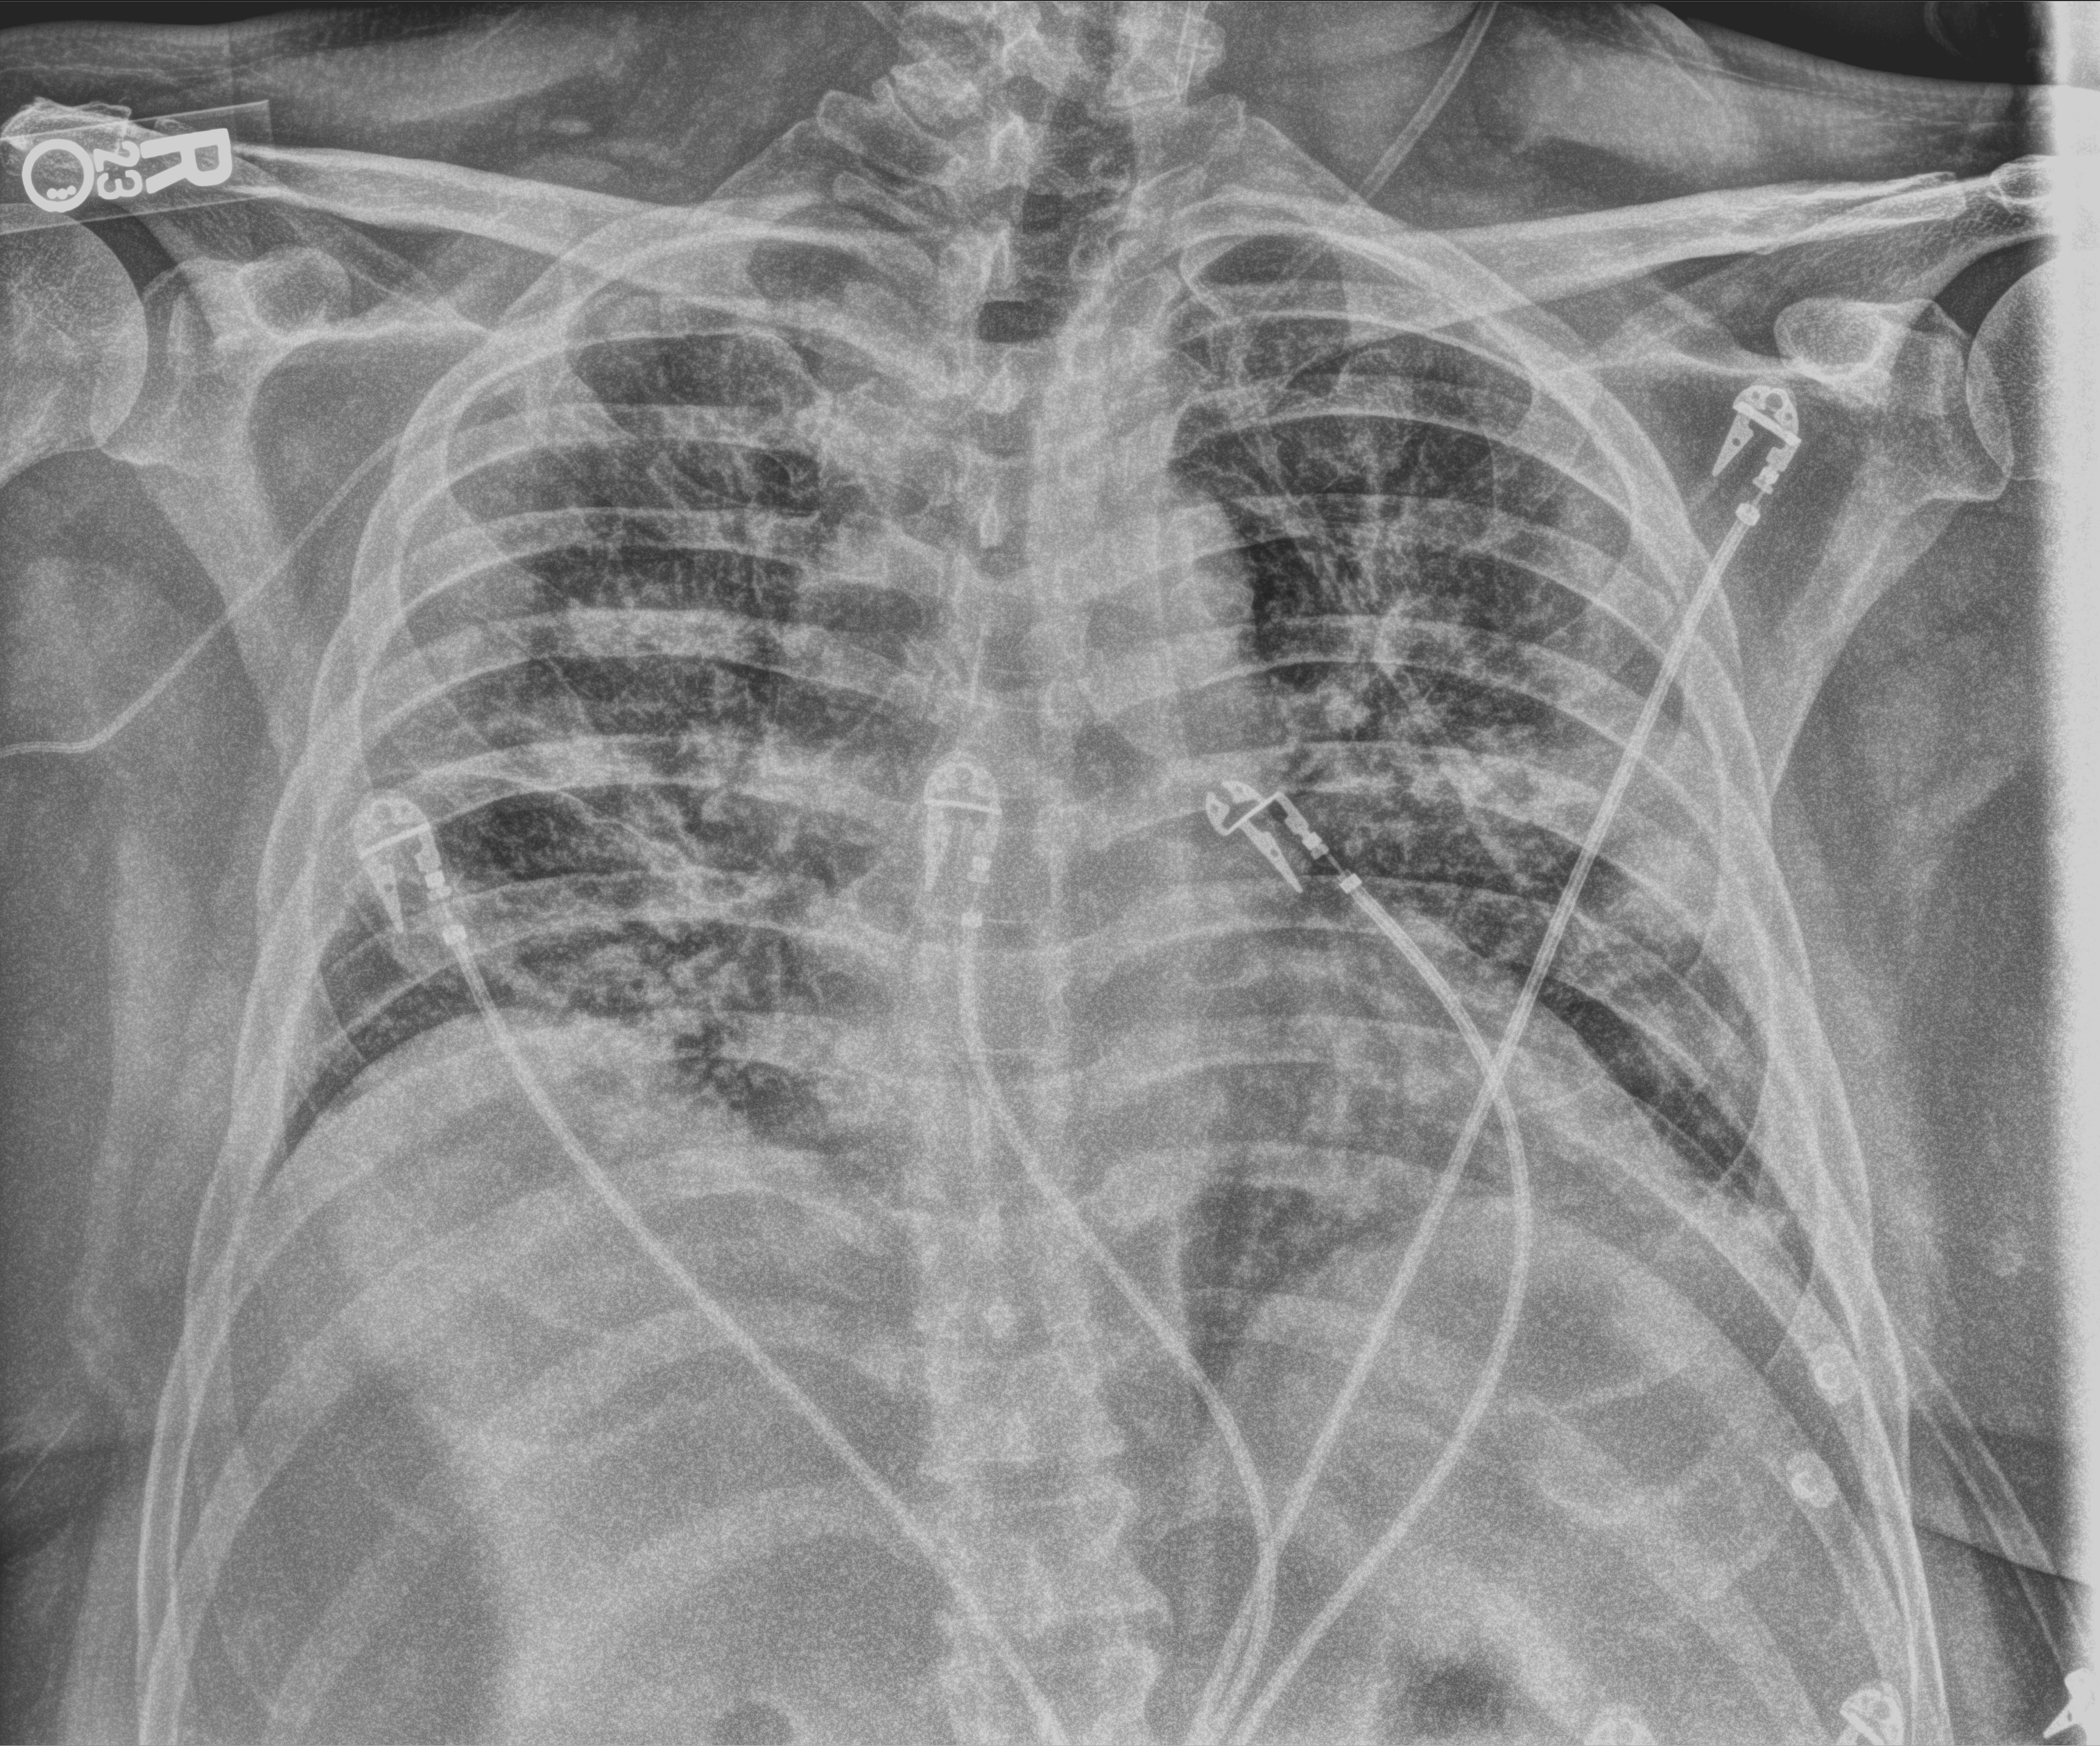
Chest X-ray (portable), anteroposterior (AP) projection. Male patient hospitalised with COVID-19, age 60–74 years.
From the hospital-stay record, not from the radiograph (when in the stay this image was taken is not recorded): mechanically ventilated during this hospital stay: no; admitted to intensive care during this hospital stay: no.